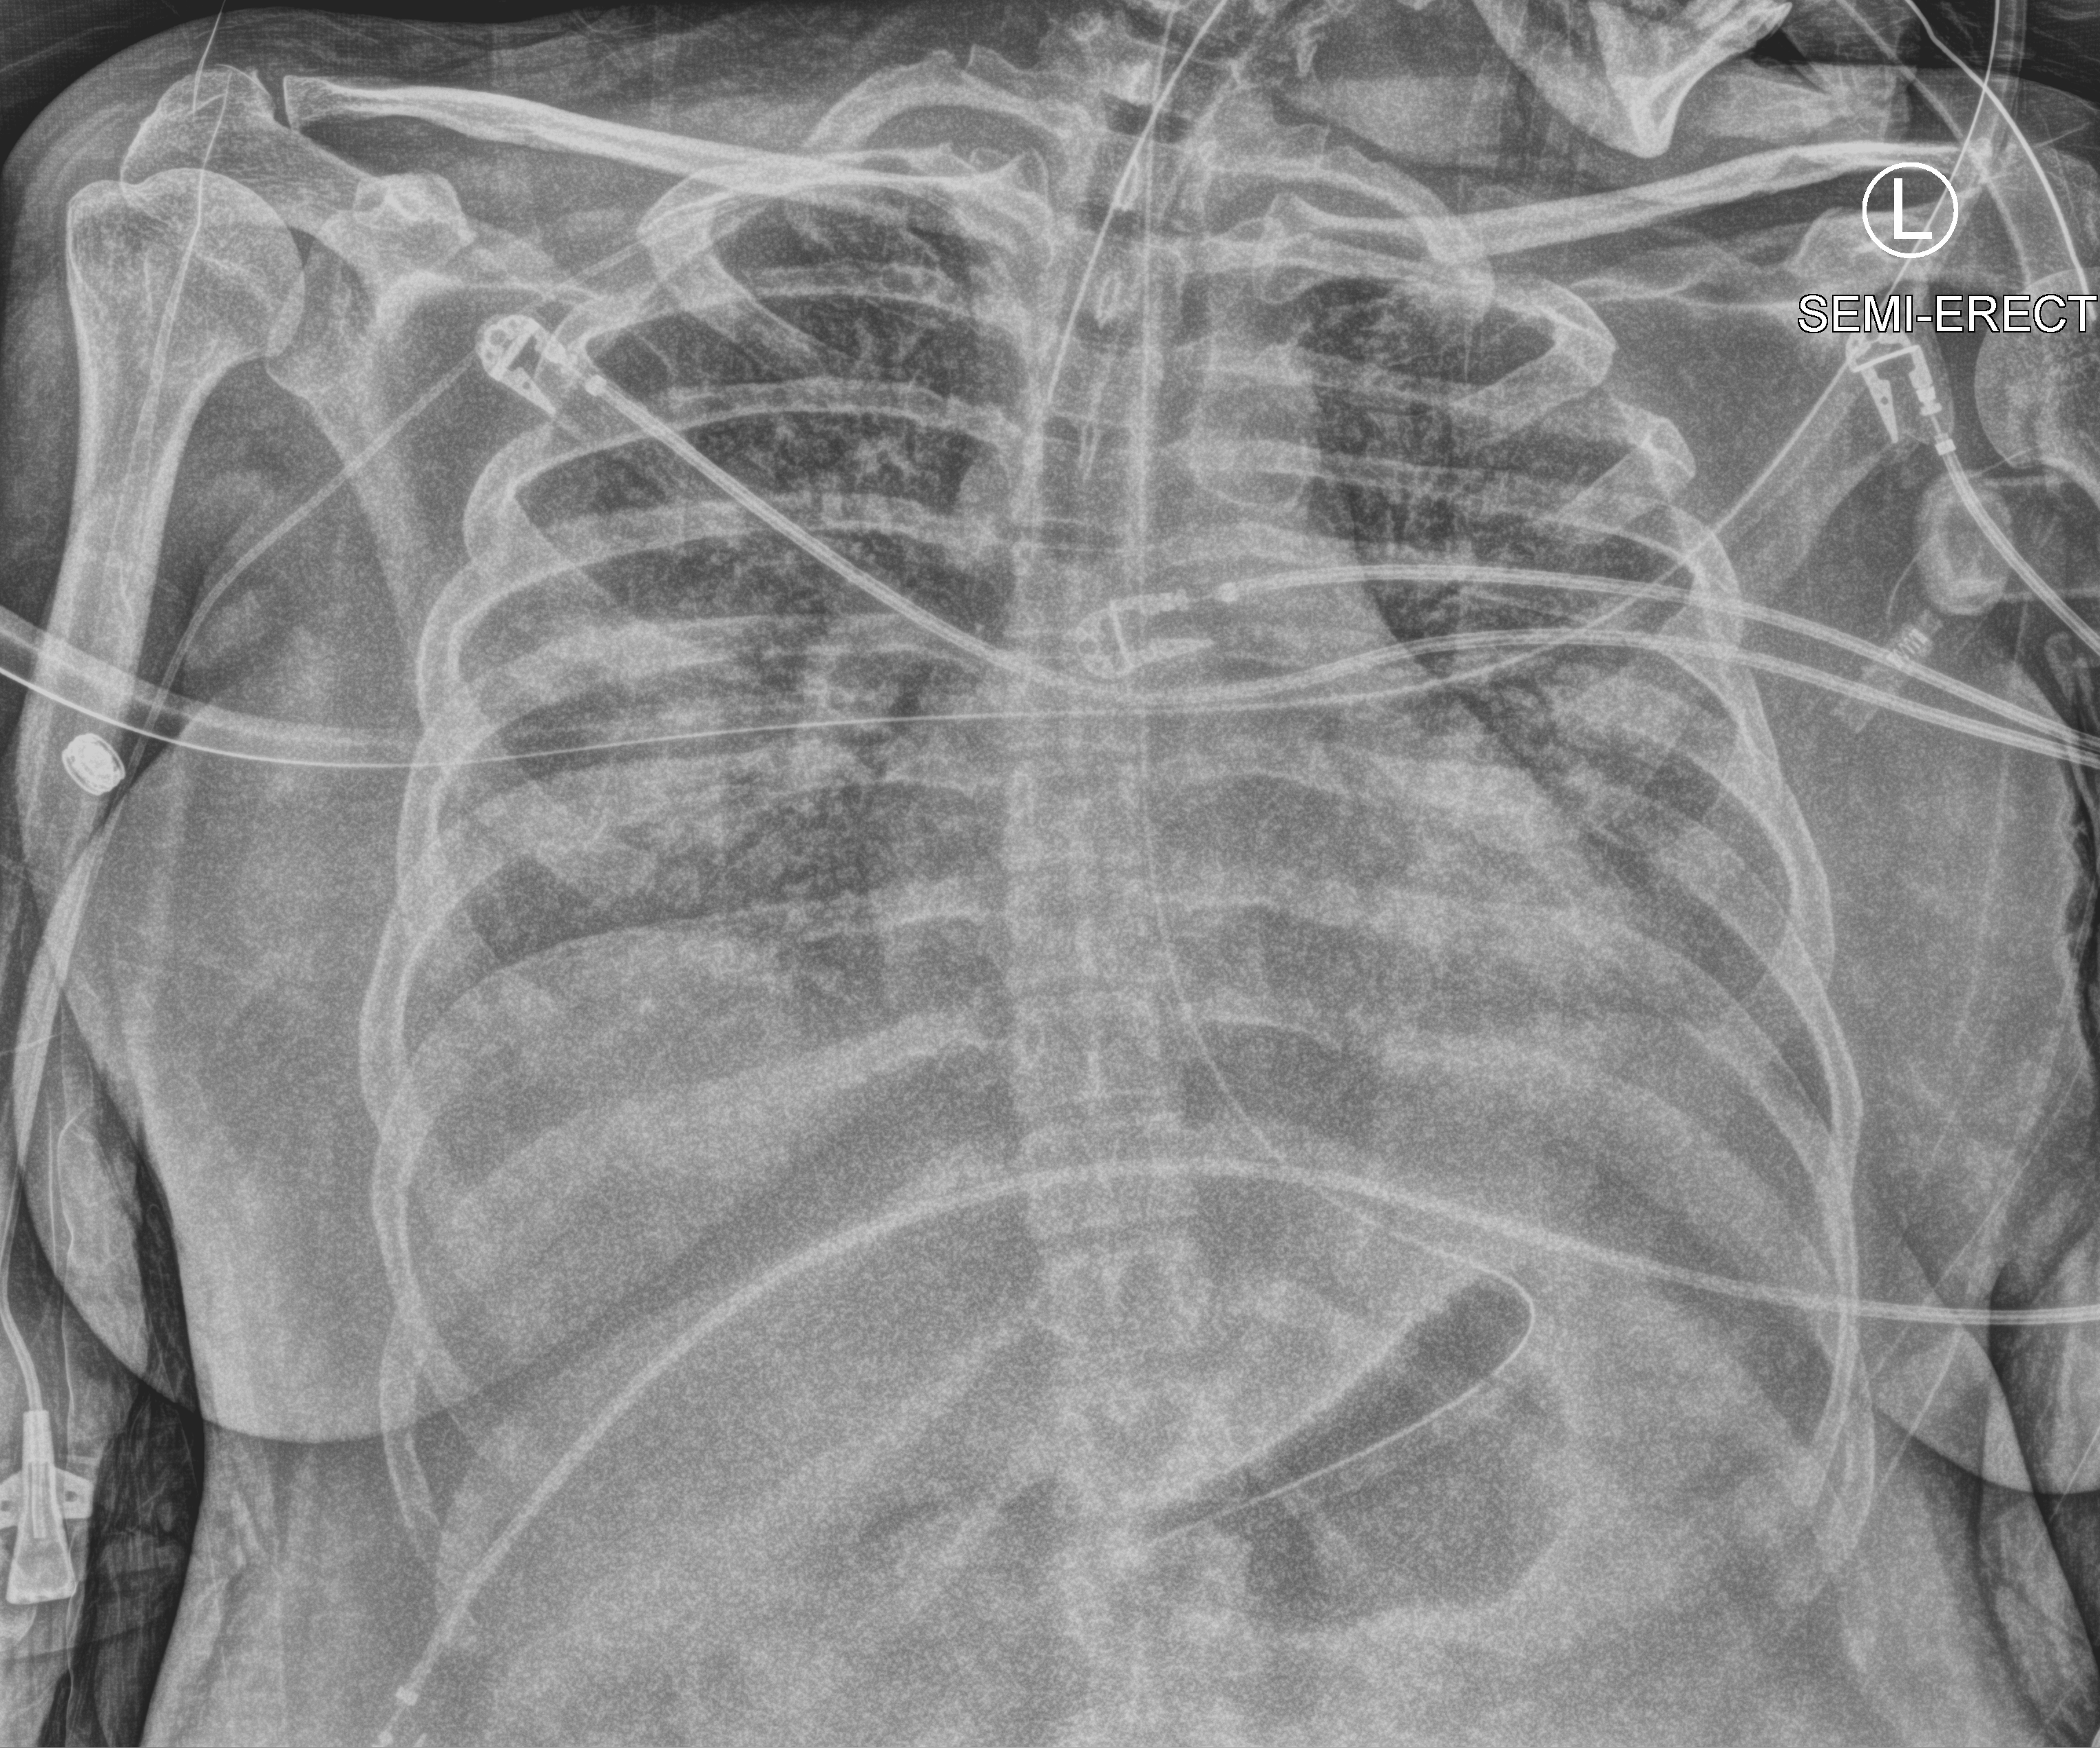
Bedside chest radiograph (computed radiography), anteroposterior (AP) projection. Patient hospitalised with COVID-19, aged 18–59 years.
Admission-level facts for this patient (not findings on this image; timing relative to this image not recorded):
- admitted to intensive care during this hospital stay: yes